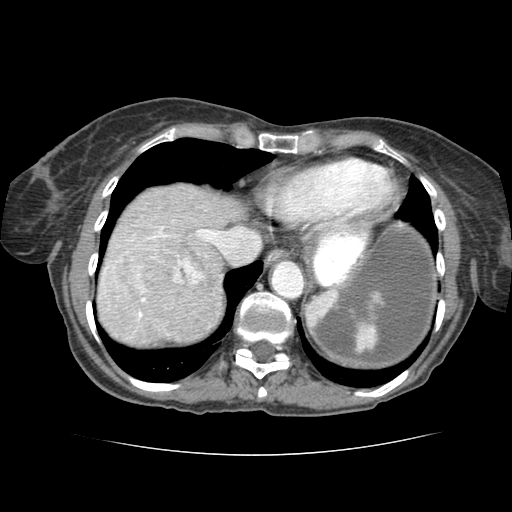
Contrast-enhanced abdominal CT (liver protocol), one axial slice. Slice 69 of 77 in the series (ordered by position). Reconstruction kernel STANDARD. Soft-tissue window (W 400 / L 40 HU). 2.5 mm slice thickness. 512 × 512 image matrix, field of view 340 × 340 mm. From the clinical record (not read from this slice): diagnosis: hepatocellular carcinoma (patient treated with transarterial chemoembolisation; whether this scan precedes or follows treatment is not stated here); TNM stage (as recorded): Stage-I; Child-Pugh class: A; tumour differentiation: well differentiated; tumour nodularity: uninodular.
Outlined on this slice (semi-automatically segmented with operator editing):
- abdominal aorta: bounding box [x1, y1, x2, y2] px = [271, 261, 303, 298]
- liver parenchyma outside the tumour (the mass and vessels are separate outlines, so this box may not span the whole liver): [100, 182, 248, 332]
- mass: [146, 256, 211, 332]
- liver vessels: [190, 271, 209, 316]